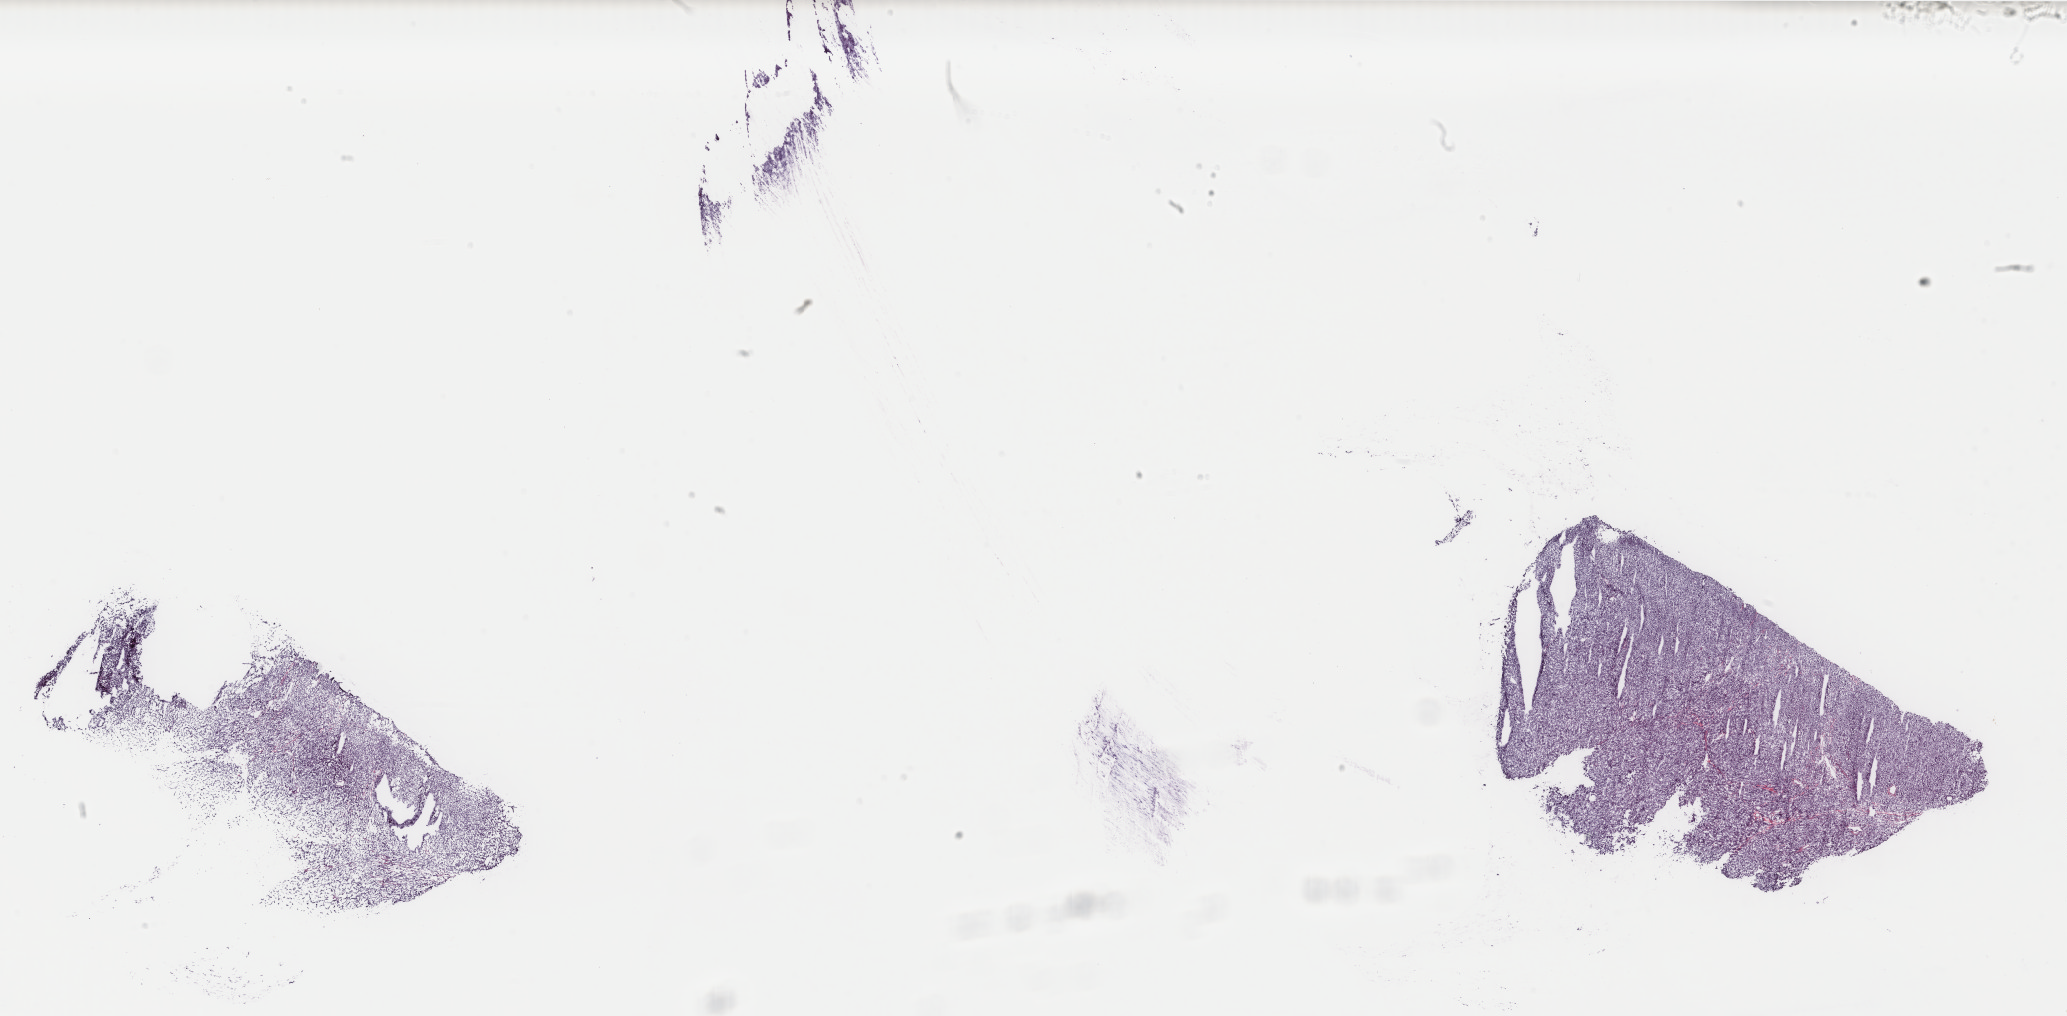
Digitized Hematoxylin and eosin (H&E) stained tissue section (whole slide), low-resolution overview of the scanned area, about 32.8 x 16.1 mm (from a 40x scan); frozen section from the top of the tissue portion; sample: primary tumour, adrenal gland. Patient: female, age at initial diagnosis 31 years. Pathologist review of this section (percent, as recorded): tumour cells 95%, tumour nuclei 100%, normal cells 0%, stromal cells 5%, necrosis 0%. Inflammatory infiltration, as recorded: lymphocyte infiltration 0%, monocyte infiltration 0%, neutrophil infiltration 0%.
Laterality: left. Diagnosis: Pheochromocytoma, NOS.